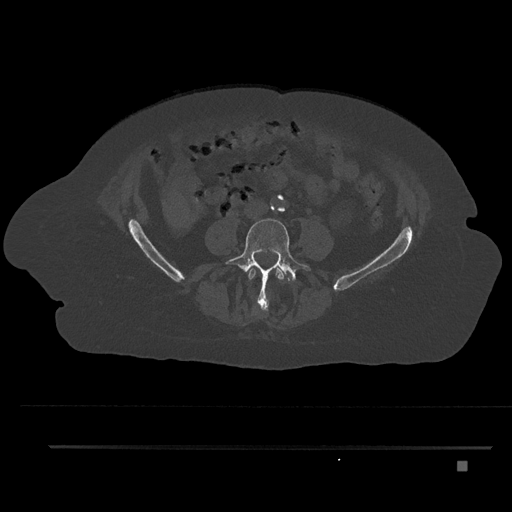
CT including the spine, one axial slice. Position 86 of 797 along the scan axis. 120 kVp. Bone window (W 1800 / L 400 HU). 0.5 mm slice thickness. 512 × 512 image matrix, field of view 437 × 437 mm. Female patient, age 76 years. From the clinical record (not read from this slice): primary cancer: lung.
Annotated regions visible in this slice (semi-automatically segmented with operator editing):
- L3 vertebra: bounding box (x1, y1, x2, y2) in pixels: (248, 268, 284, 310)
- L4 vertebra: (223, 218, 311, 311)
- L5 vertebra: (289, 273, 295, 281)